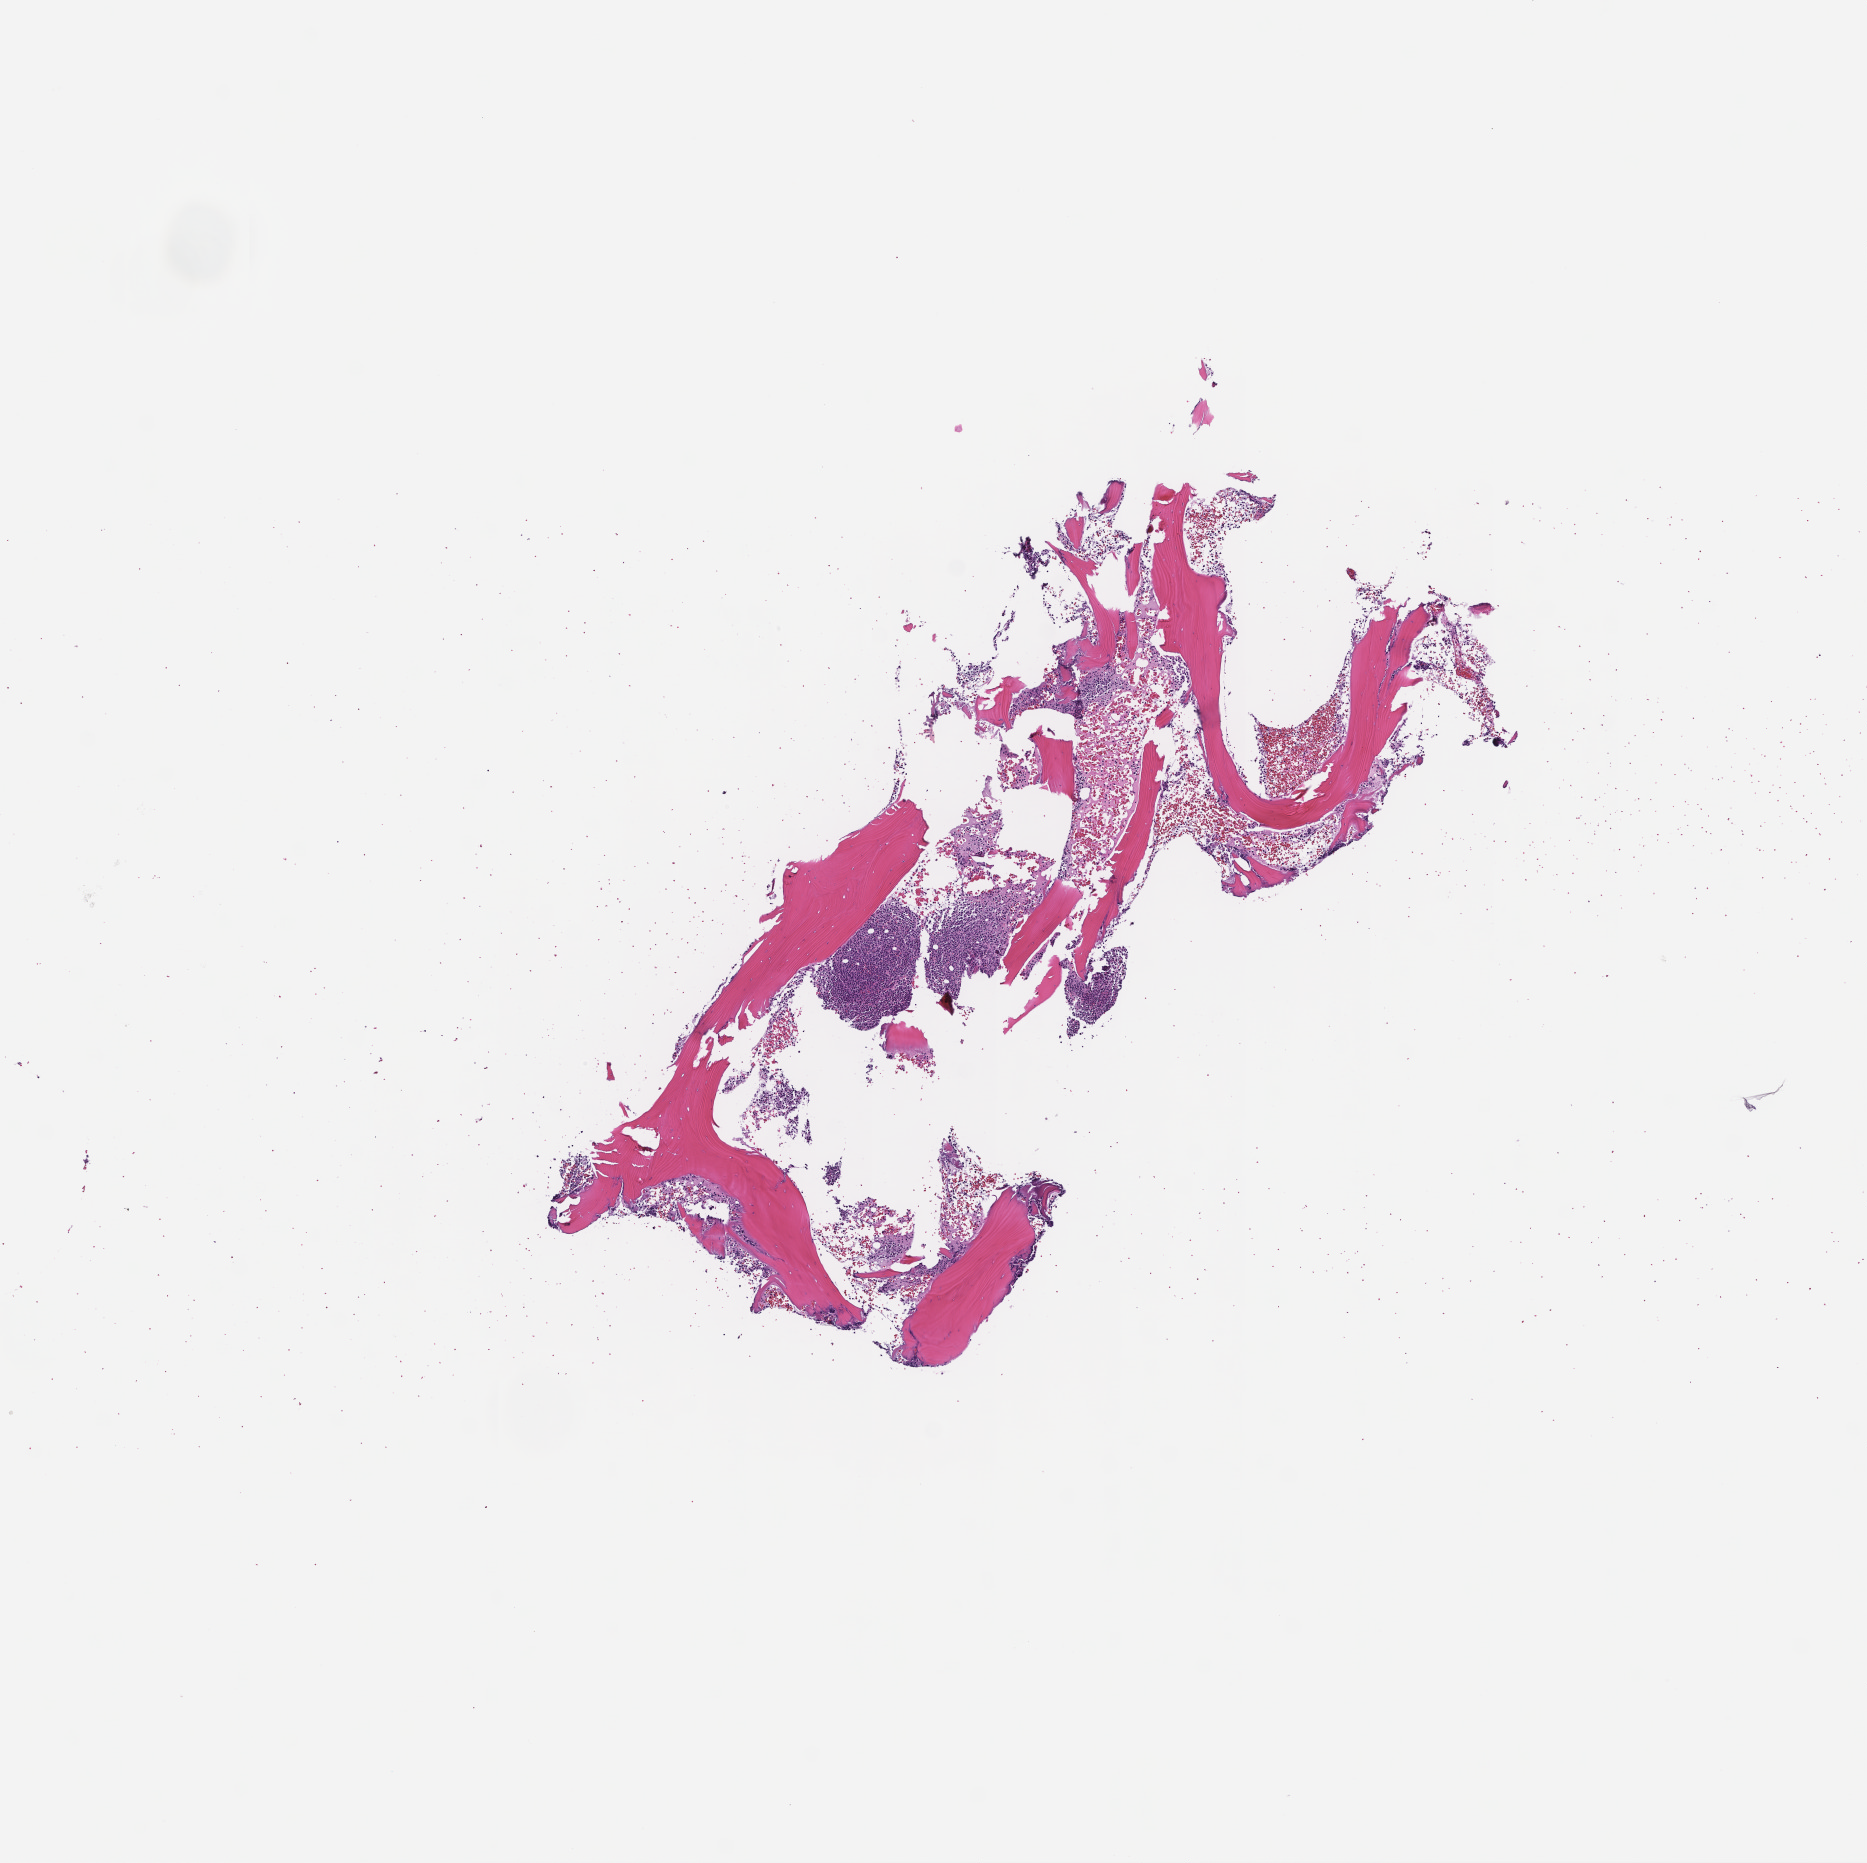
H&E whole-slide image — whole scanned area (about 7.5 x 7.5 mm) shown as a low-resolution overview; FFPE section; site: bone marrow; collected at baseline (before treatment). Patient: male.
This section: primary tumor. Diagnosis: Plasma Cell Myeloma.